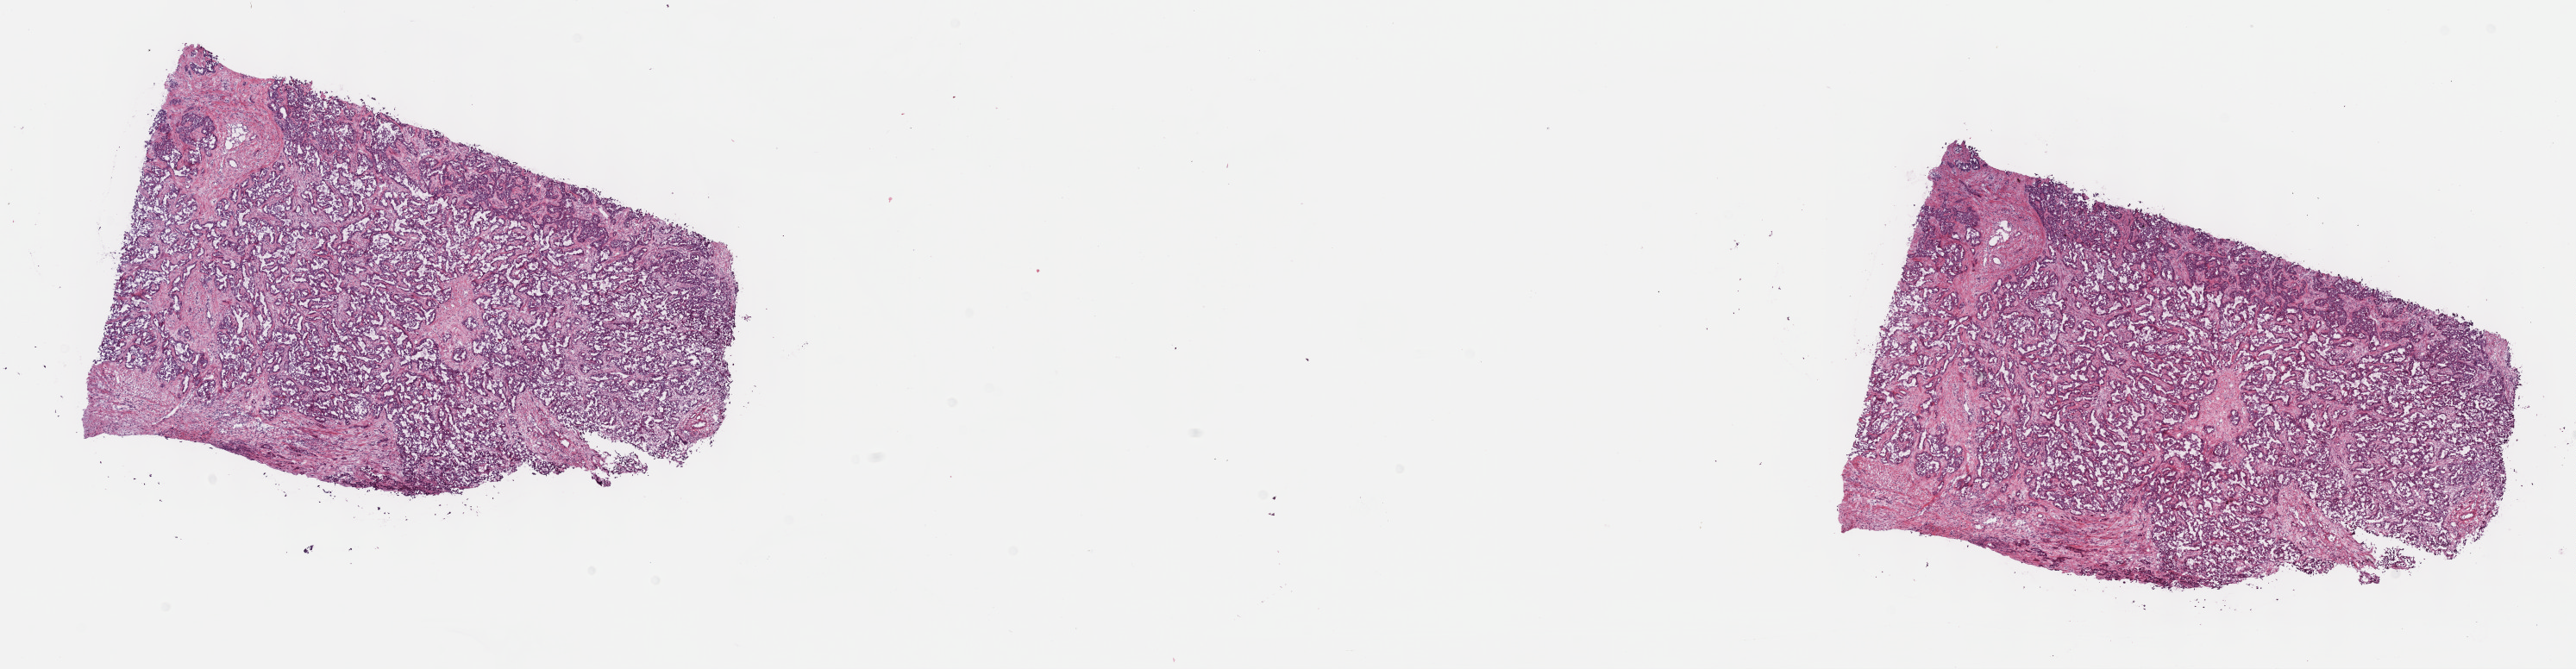
H&E-stained whole-slide image — shown as a low-resolution overview of the whole scanned area (about 24.2 x 6.3 mm, acquisition: 40x scan). Frozen section from the top of the tissue portion. Primary tumour sample from the bile duct. Female, age 62 years at initial diagnosis. Histologic grade: G3 (poorly differentiated). Composition of this section per pathologist review: tumour cells 100%, tumour nuclei 70%, normal cells 0%, stromal cells 0%, necrosis 0%. Inflammatory infiltration, as recorded: lymphocyte infiltration 2%, monocyte infiltration 0%, neutrophil infiltration 0%.
AJCC pathologic stage: I (7th edition). Pathologic diagnosis: Cholangiocarcinoma (intrahepatic bile duct).